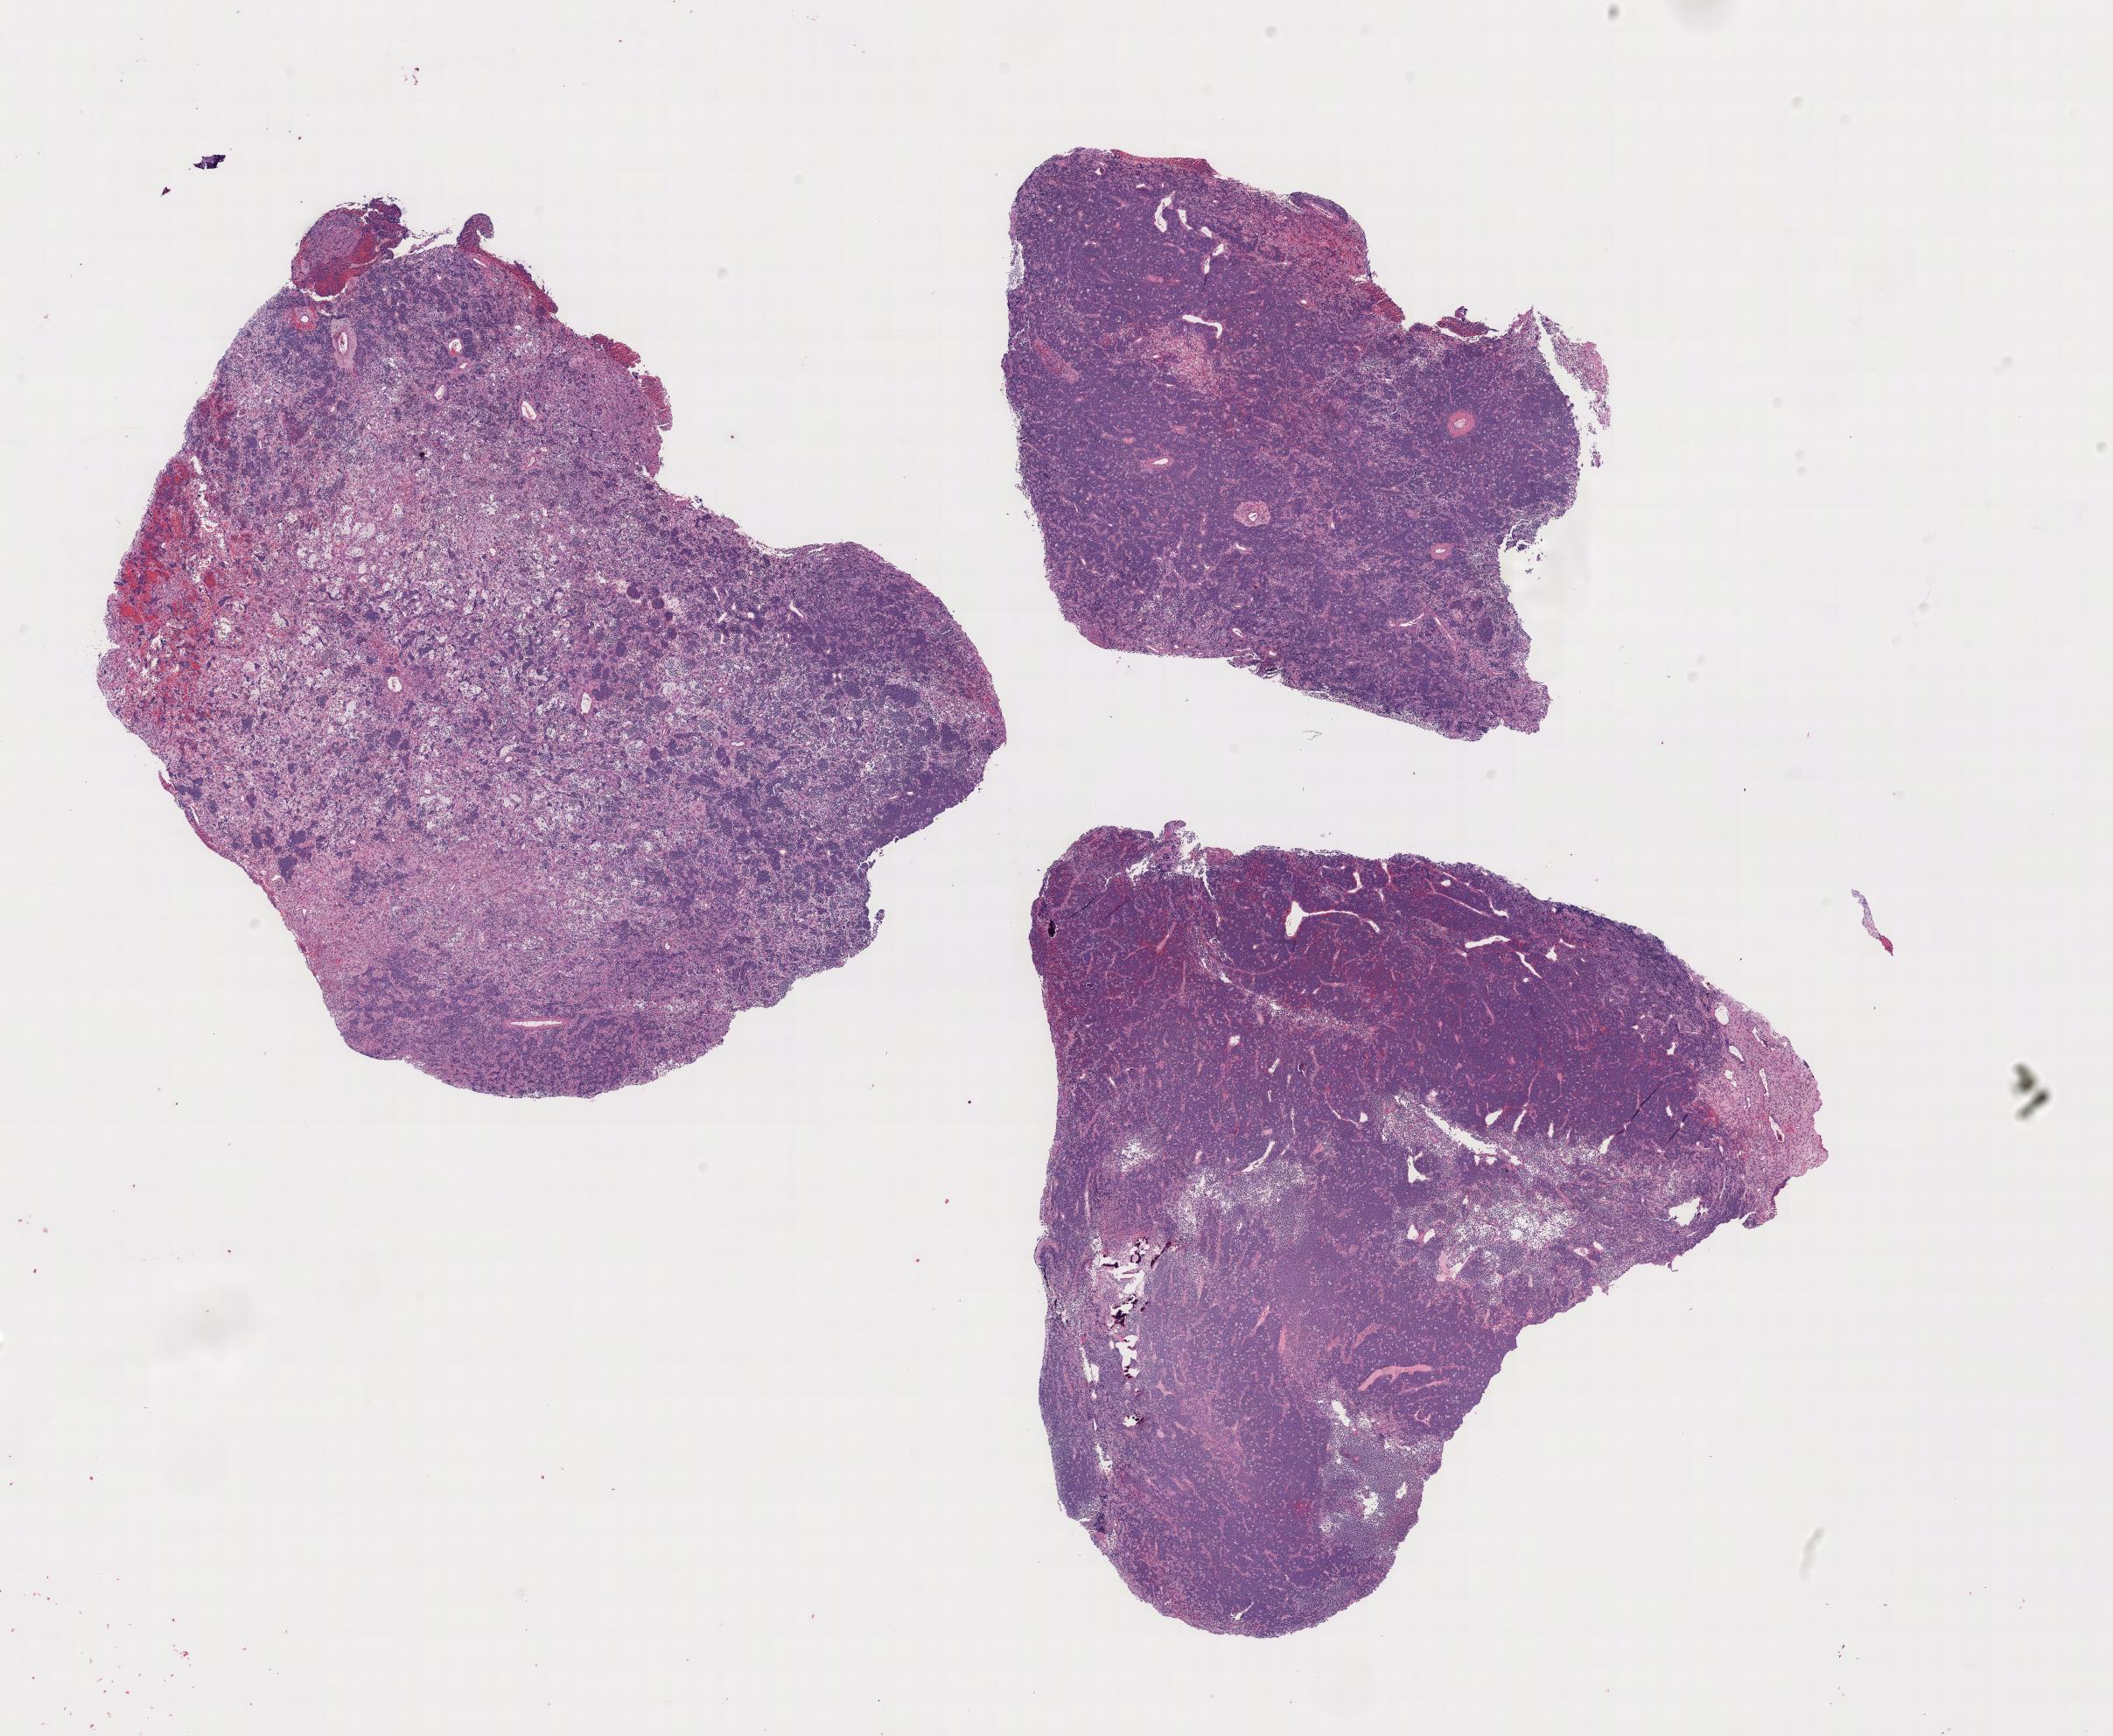
Whole-slide image, haematoxylin and eosin stain, shown as a low-resolution overview of the whole scanned area. Tumor tissue. Site: cranium. Male, age 5 years at initial diagnosis.
Histologic diagnosis: Burkitt lymphoma, NOS.